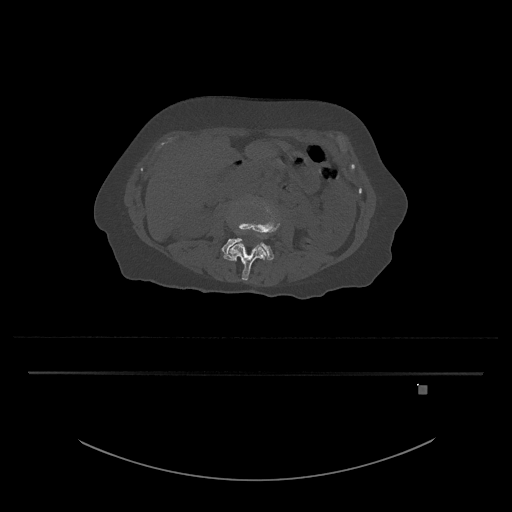
CT including the spine, one axial slice. Position 403 of 797 along the scan axis. Reconstruction kernel Br40s/3. Bone window (W 1800 / L 400 HU). 512 × 512 image matrix, field of view 500 × 500 mm. Patient: female, 57 years. Case-level facts recorded for this patient, not image findings: primary cancer: cervical.
Outlined on this slice (semi-automatic segmentation, software-assisted and operator-edited):
- L3 vertebra: box from (x=223, y=204) to (x=280, y=281) px
- L4 vertebra: (x=221, y=238)–(x=274, y=261)